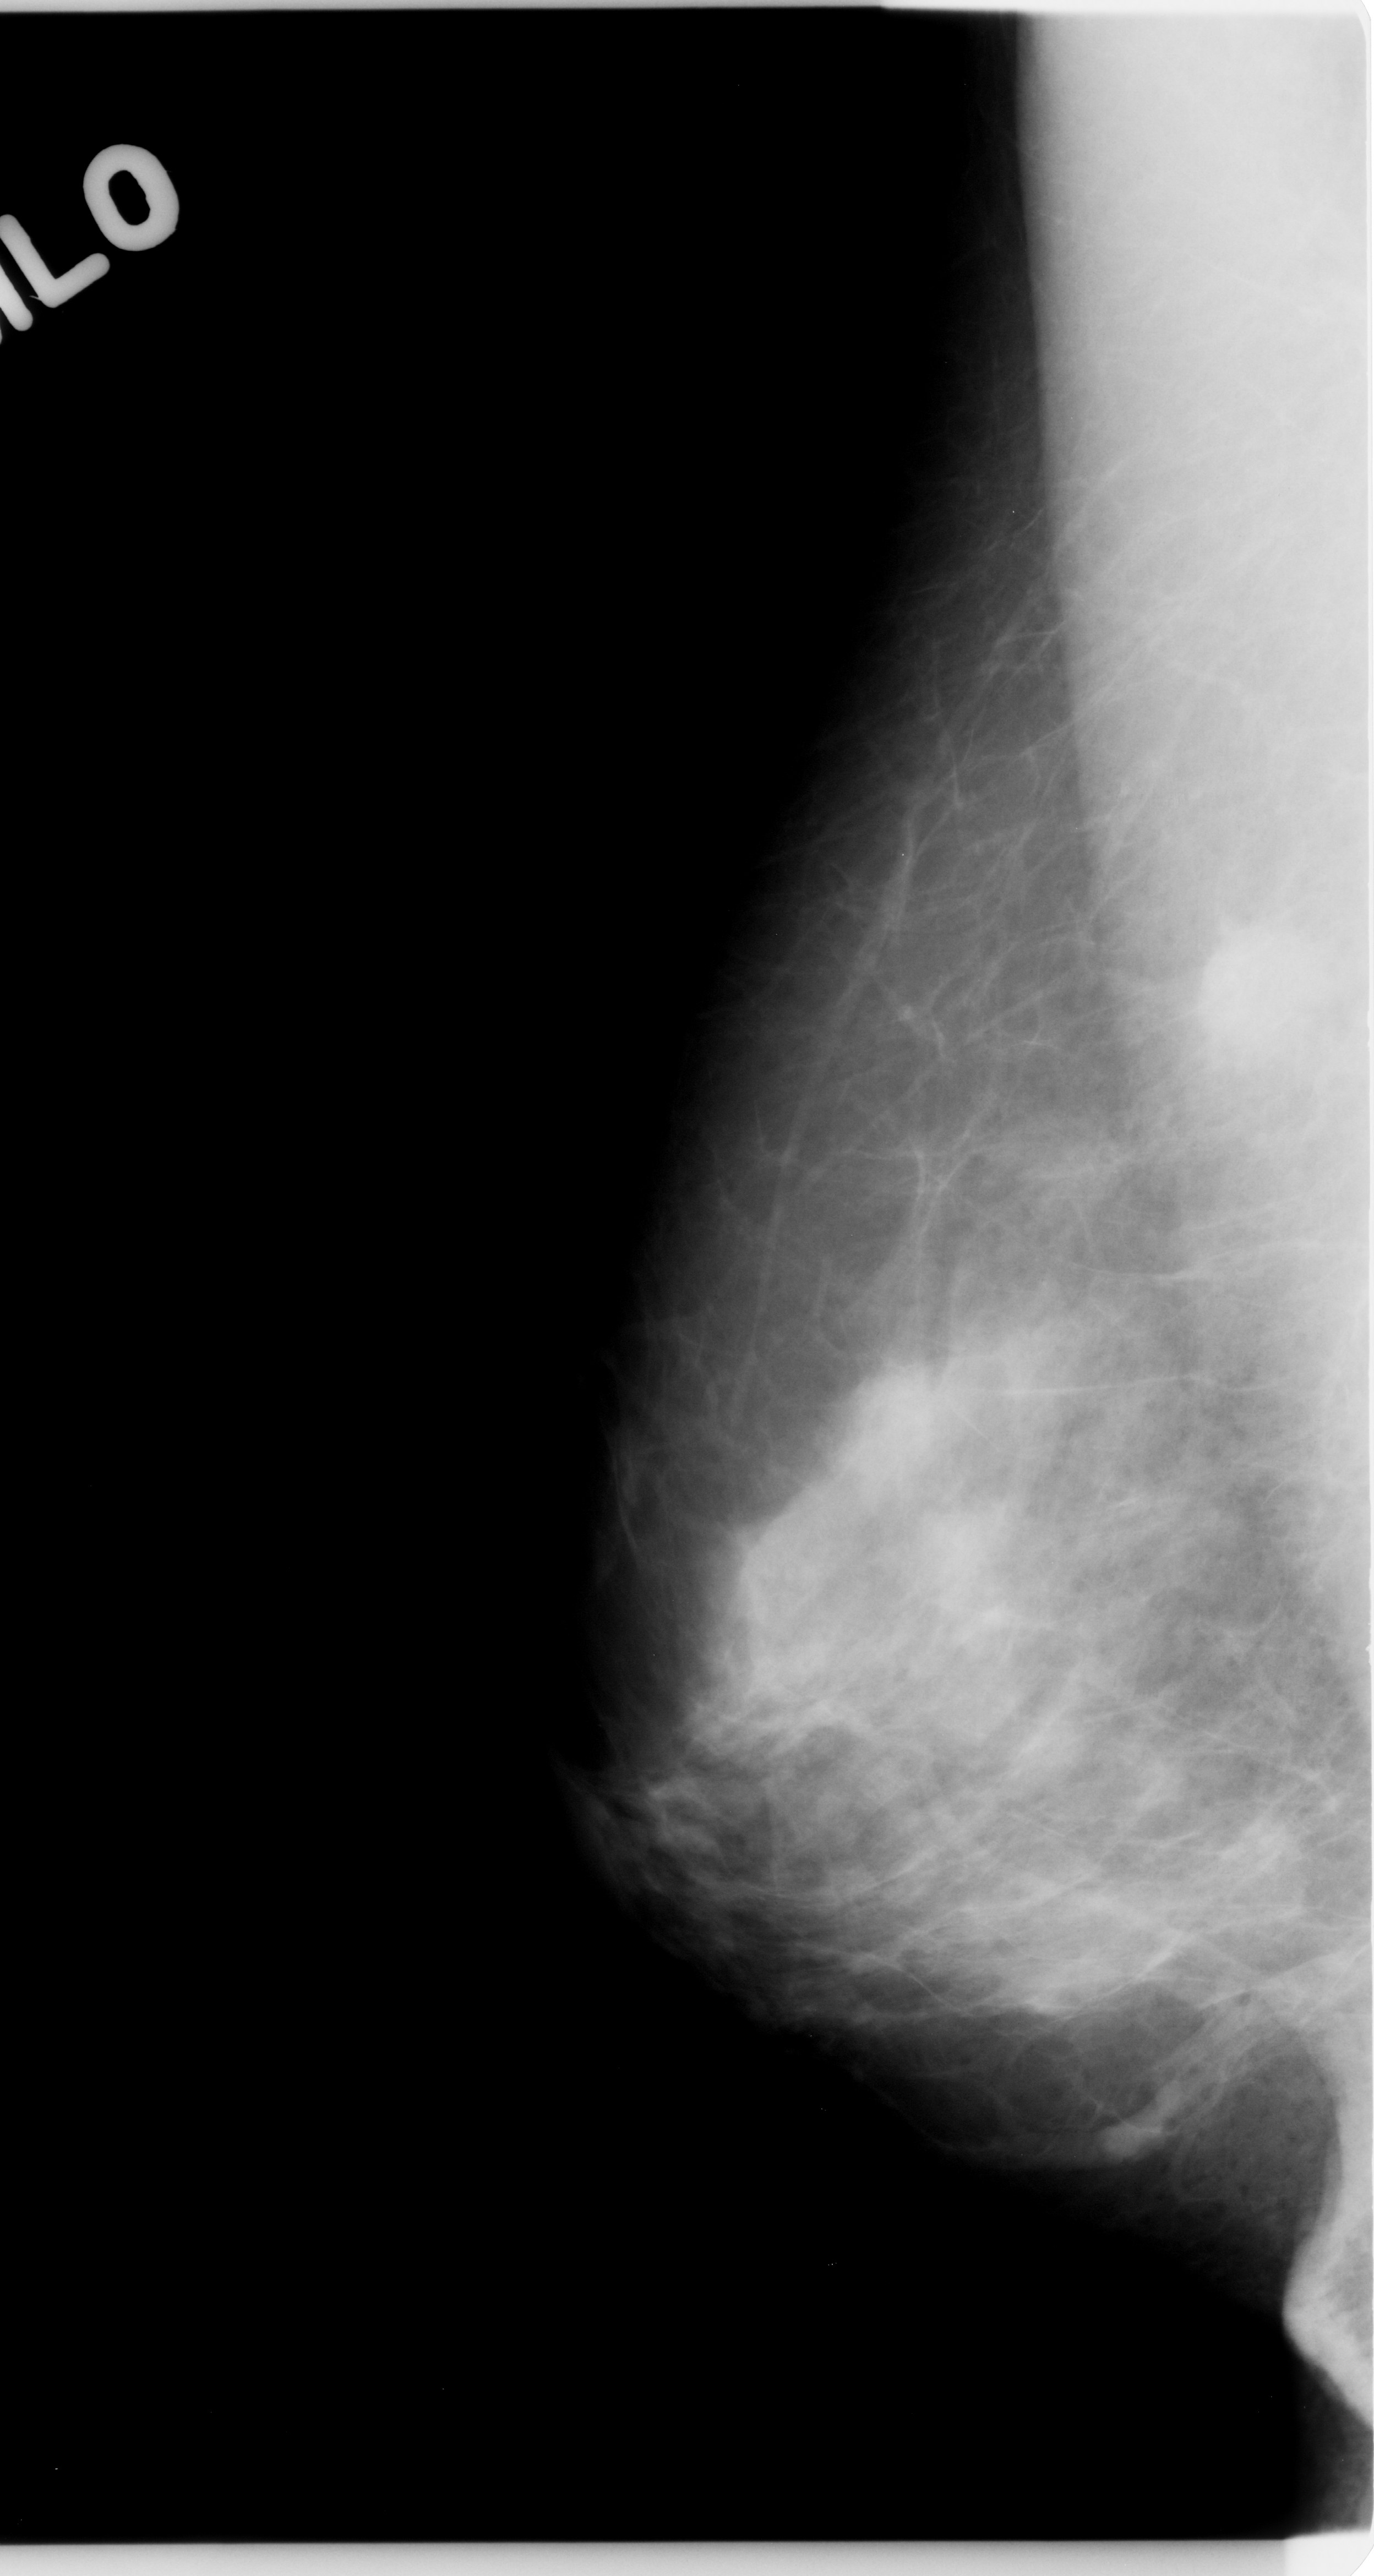
Digitized screen-film mammogram. Right breast. MLO view. BI-RADS breast density category 2 (scale 1–4). 1374 × 2576 image matrix.
Expert-marked regions of interest on this image (one box per marked abnormality):
- mass, shape round, margins spiculated; BI-RADS assessment category 5; subtlety rating 5 on a 1 (subtle) to 5 (obvious) scale; pathology result (as recorded, not read from the image): malignant: box from (x=1163, y=899) to (x=1322, y=1077) px